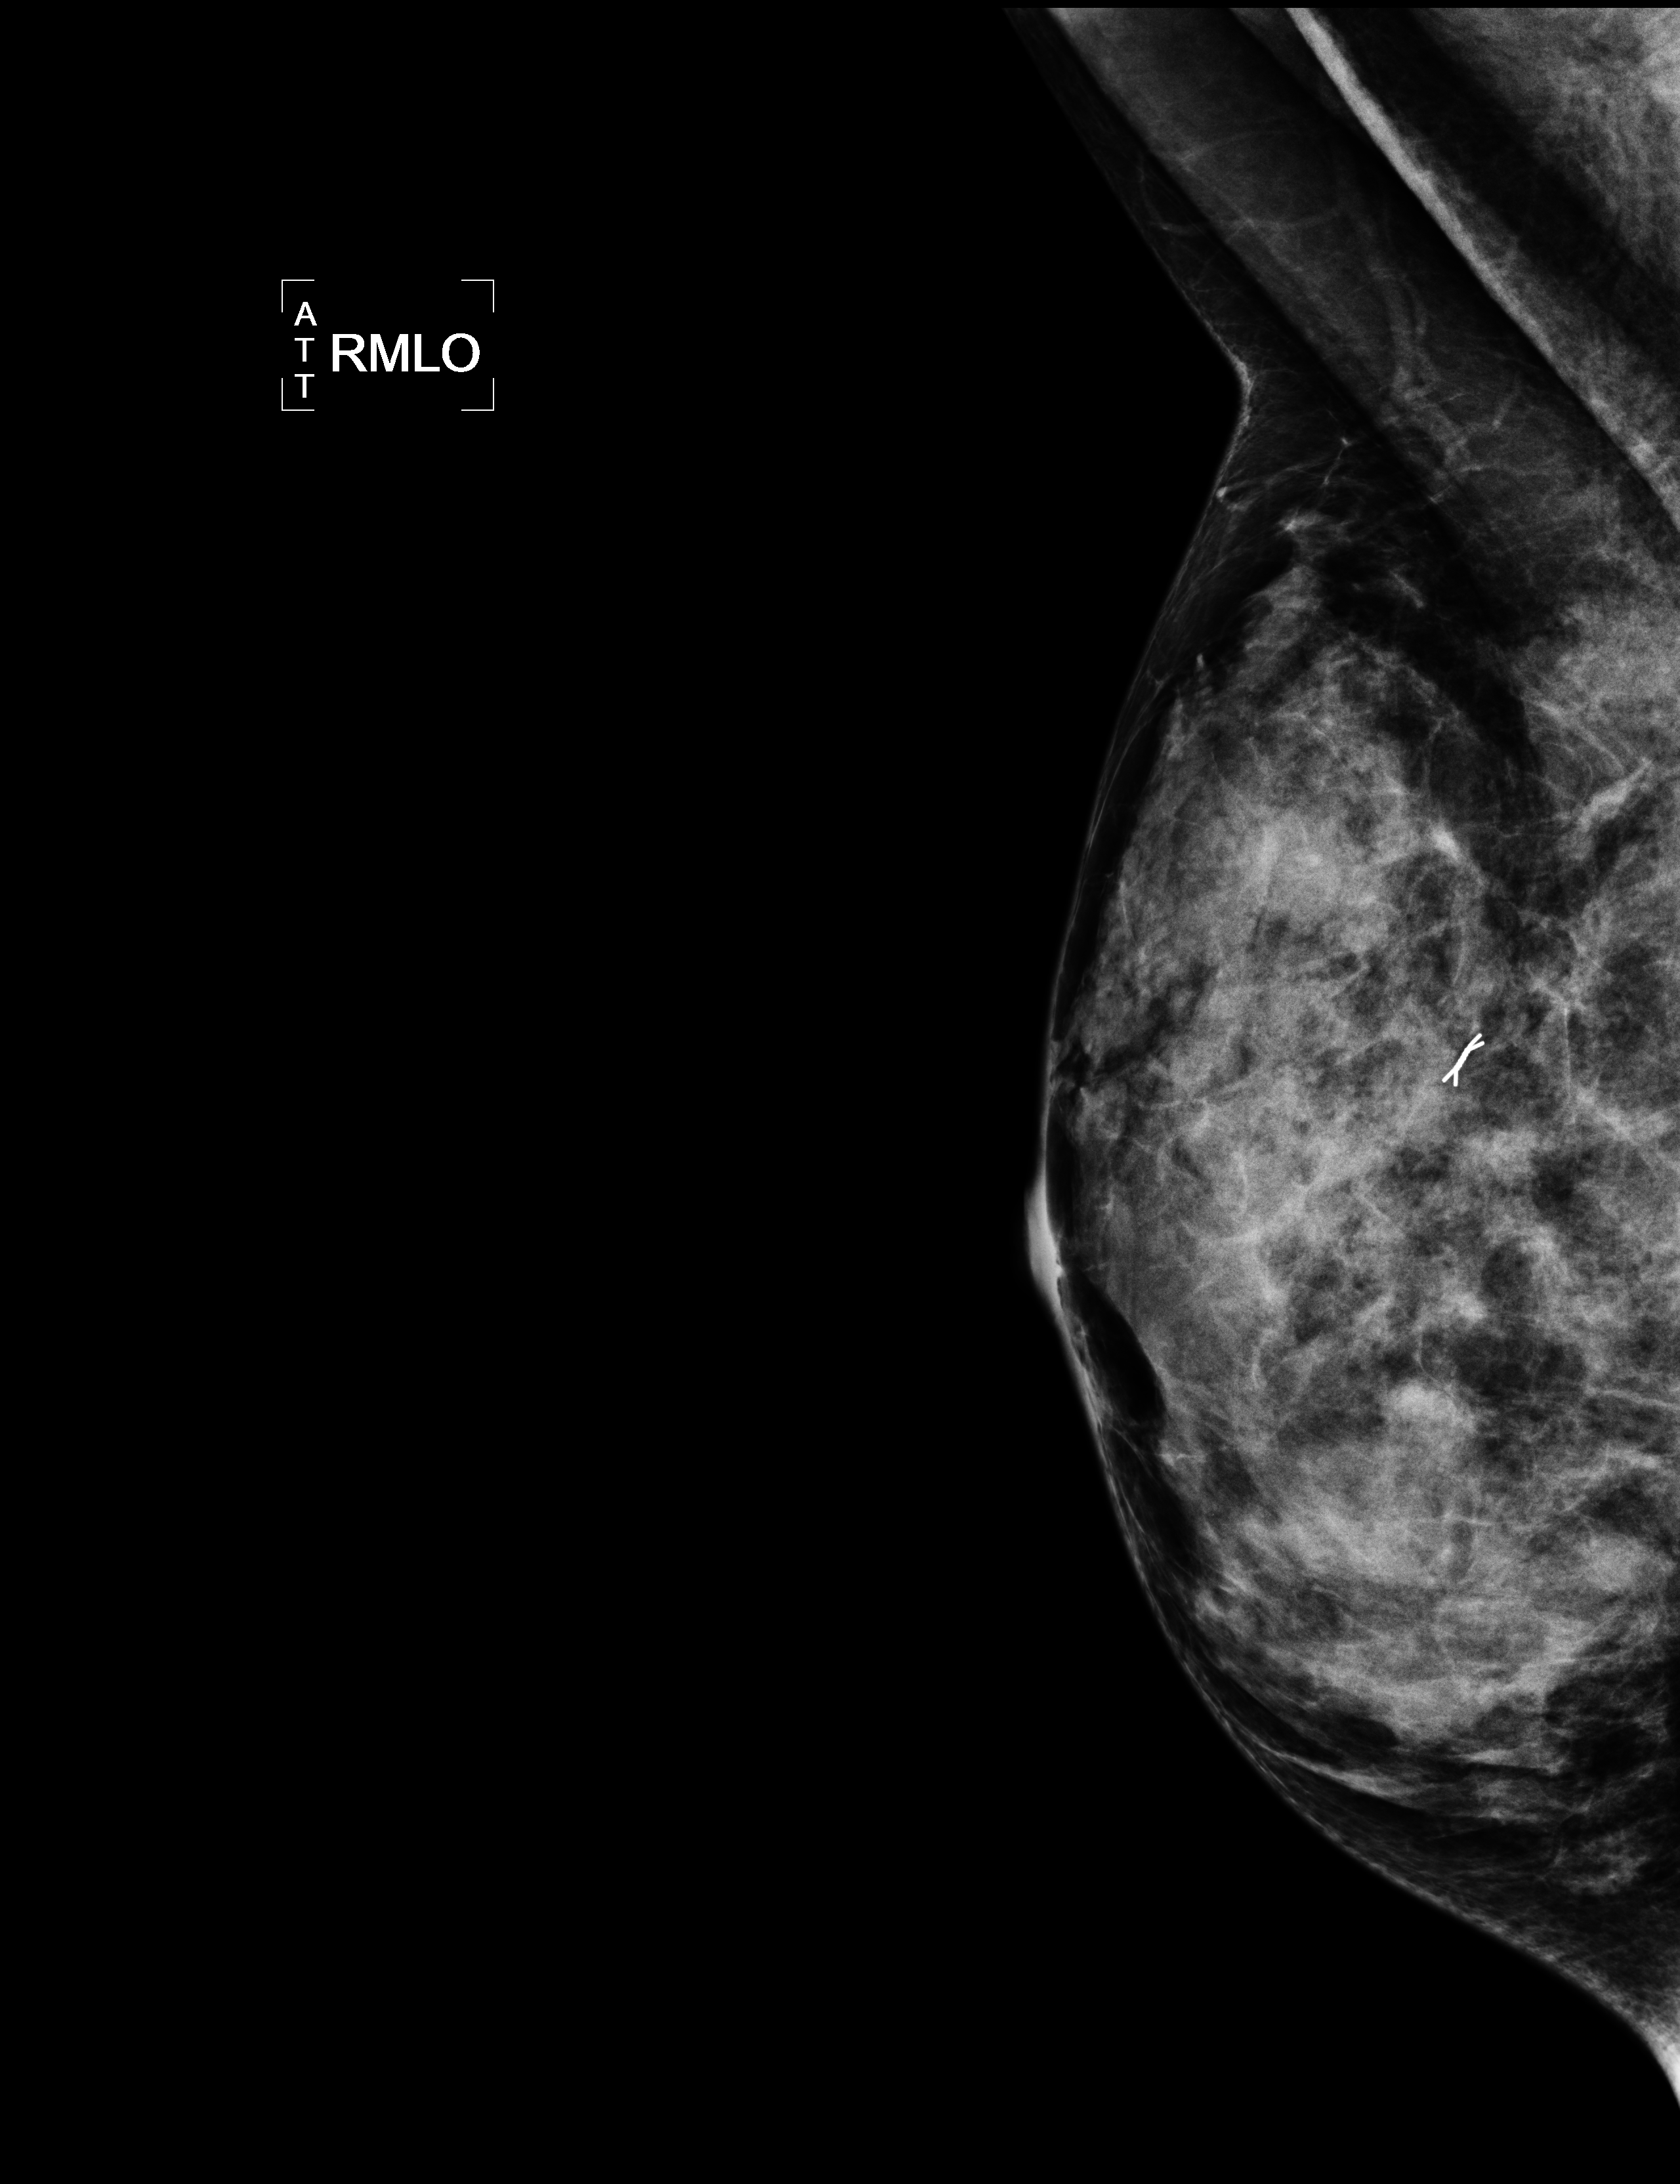
Mammogram, right breast, MLO view.
Pathology recorded for this patient (not read from this image): pathology diagnosis: Invasive ductal carcinoma, modified Scarff-Bloom-Richardson grade II/III. No intraductal carcinoma component seen. (right breast); receptor status (as recorded): ER pos (strong), PR pos (strong), HER2 neg (weak); Ki-67 (as recorded): pos (strong); clinical background (as recorded): late 20's y.o. with bx-proven CA.